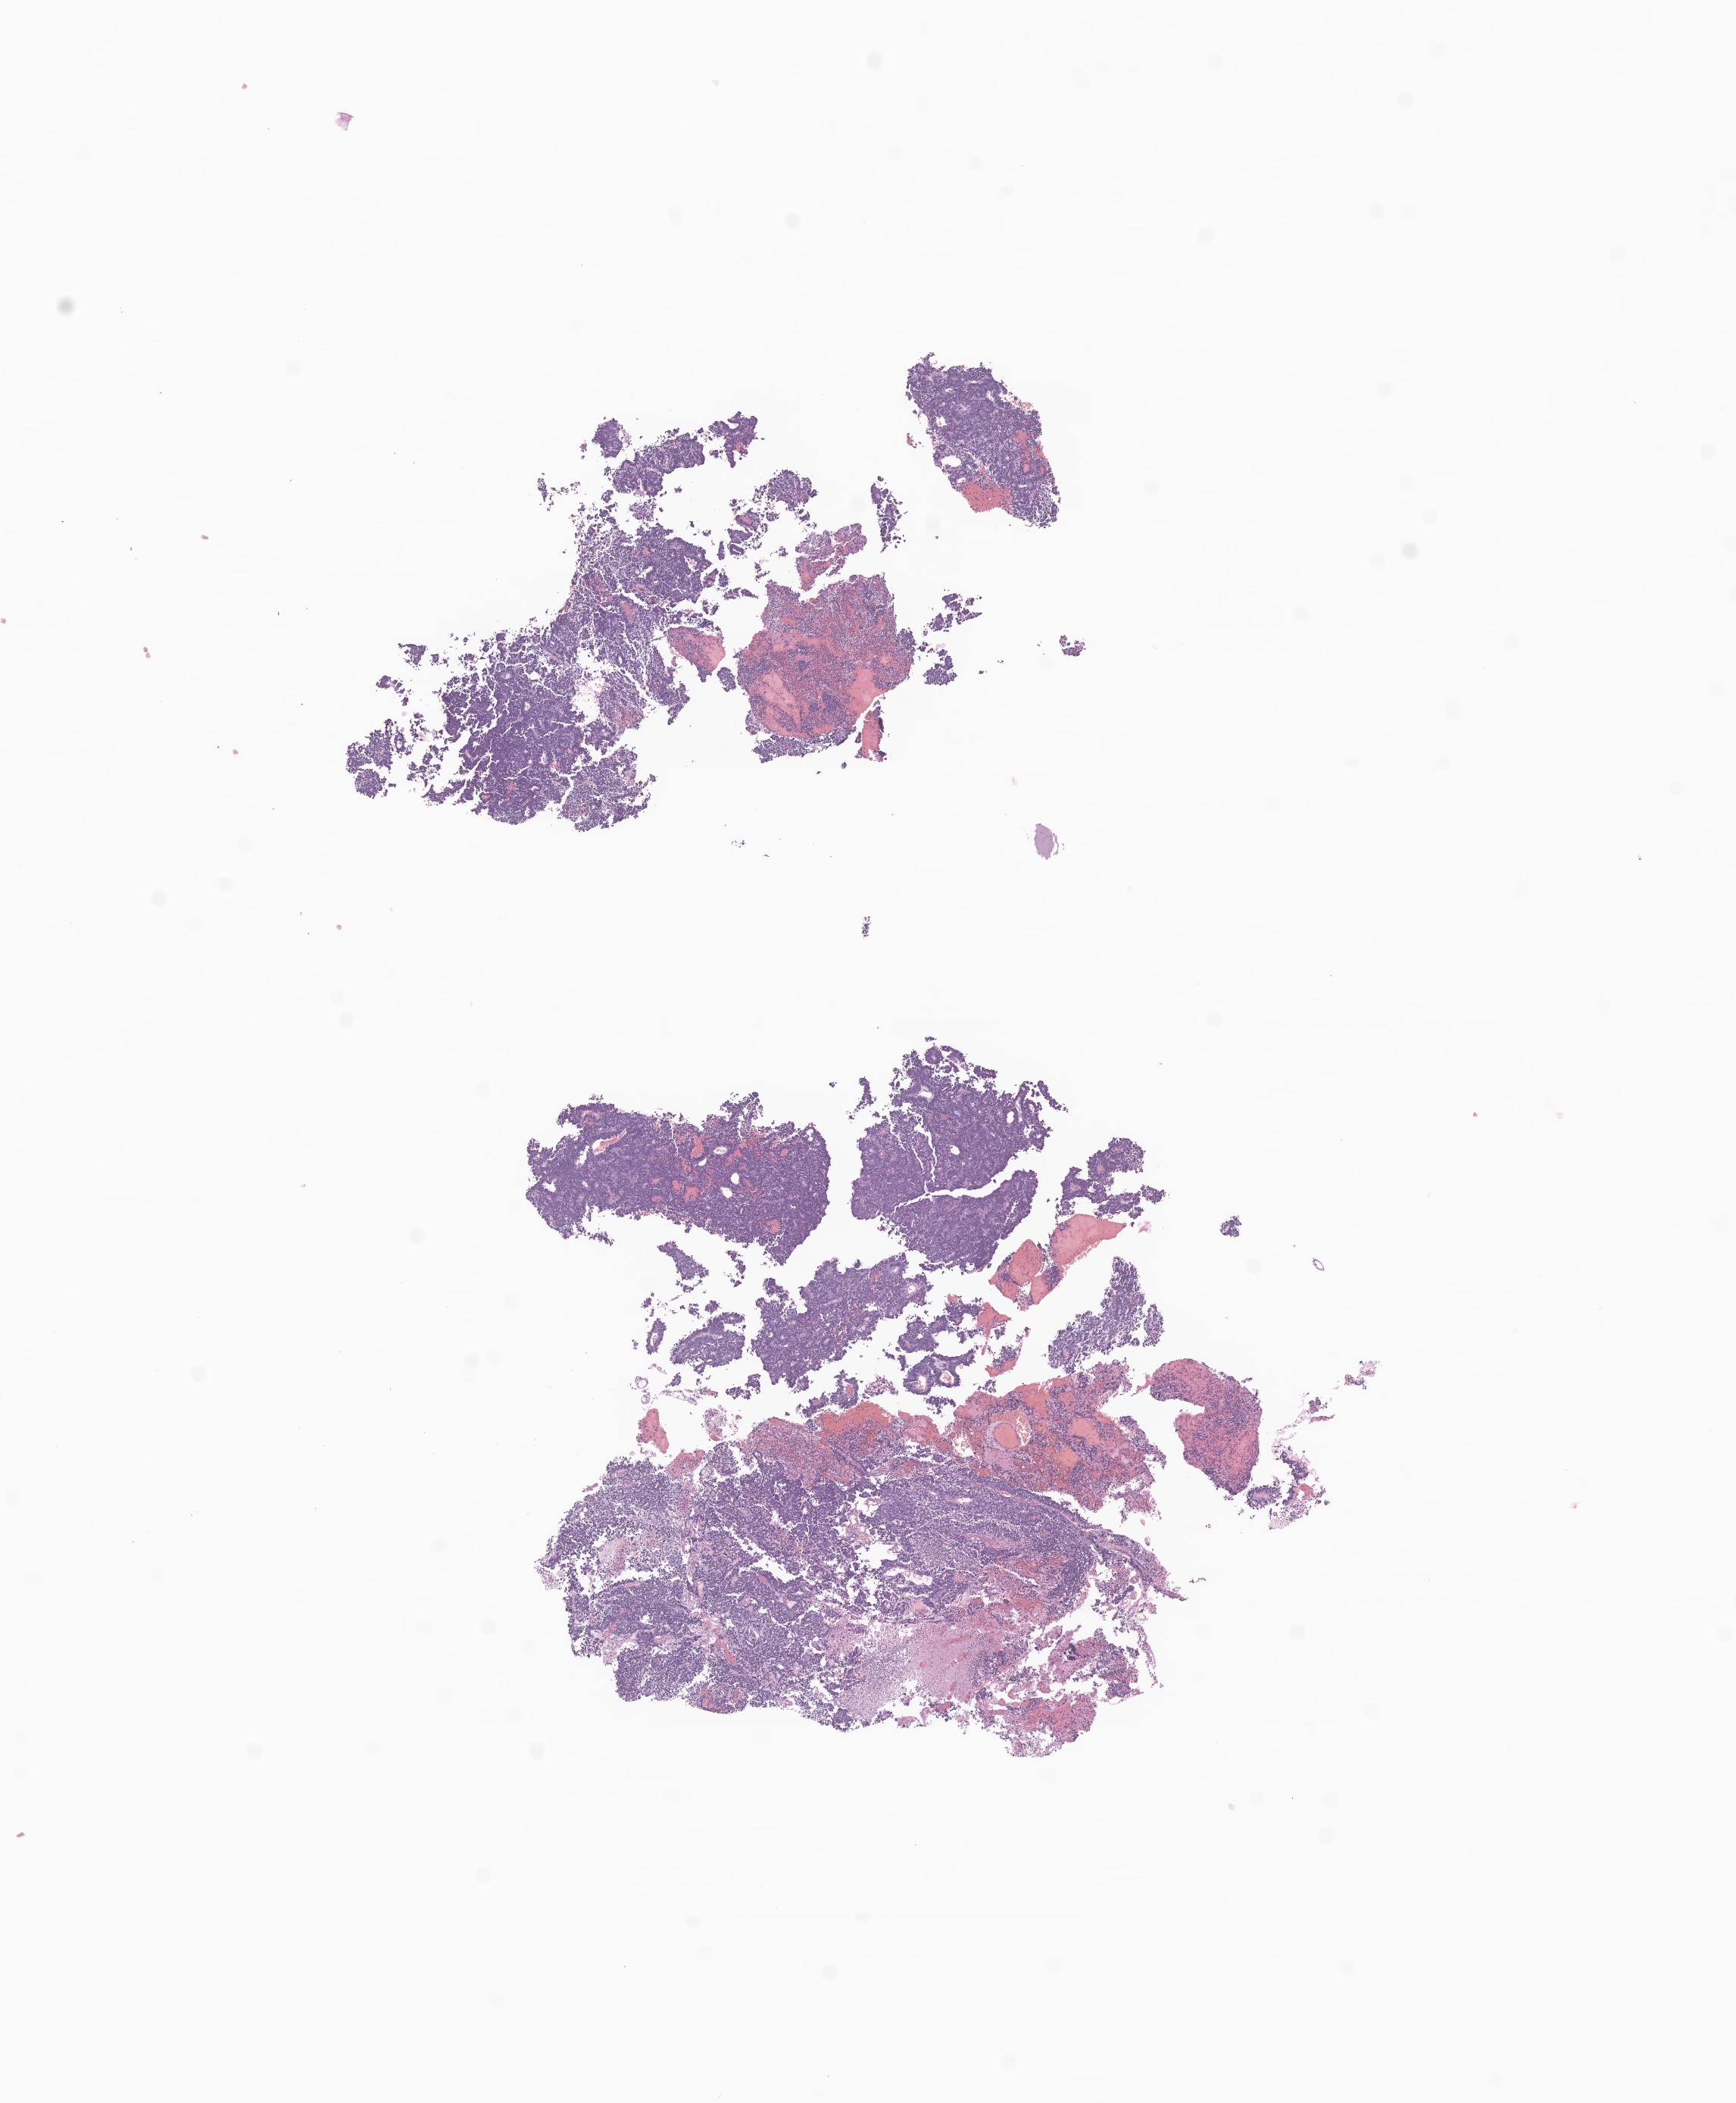
Whole-slide image, hematoxylin and eosin (H&E) stain of tumor tissue from the brain, whole scanned area (about 9.7 x 11.7 mm) shown as a low-resolution overview; formalin-fixed, paraffin-embedded (FFPE) tissue. Patient female; age 960 days (about 2.6 years).
- diagnosis (ICD-O-3 morphology term): Tumor cells, malignant